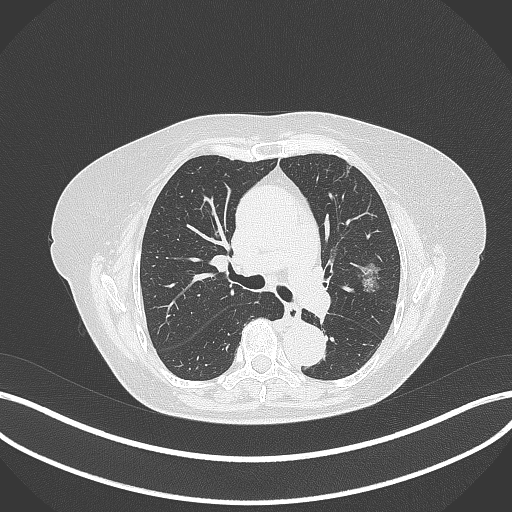
Chest CT, one axial slice. Position 204 of 316 along the scan axis. Lung window (W 1500 / L -600 HU). 1 mm slice thickness. 512 × 512 image matrix. Patient: female, 75 years. From the clinical record (not read from this slice): clinical TNM (as recorded): T1c N0 M0.
Outlined on this slice (bounding box drawn by a radiologist):
- lung tumour (recorded histology: adenocarcinoma): bounding box <352,260,385,296> (left, top, right, bottom; pixels)